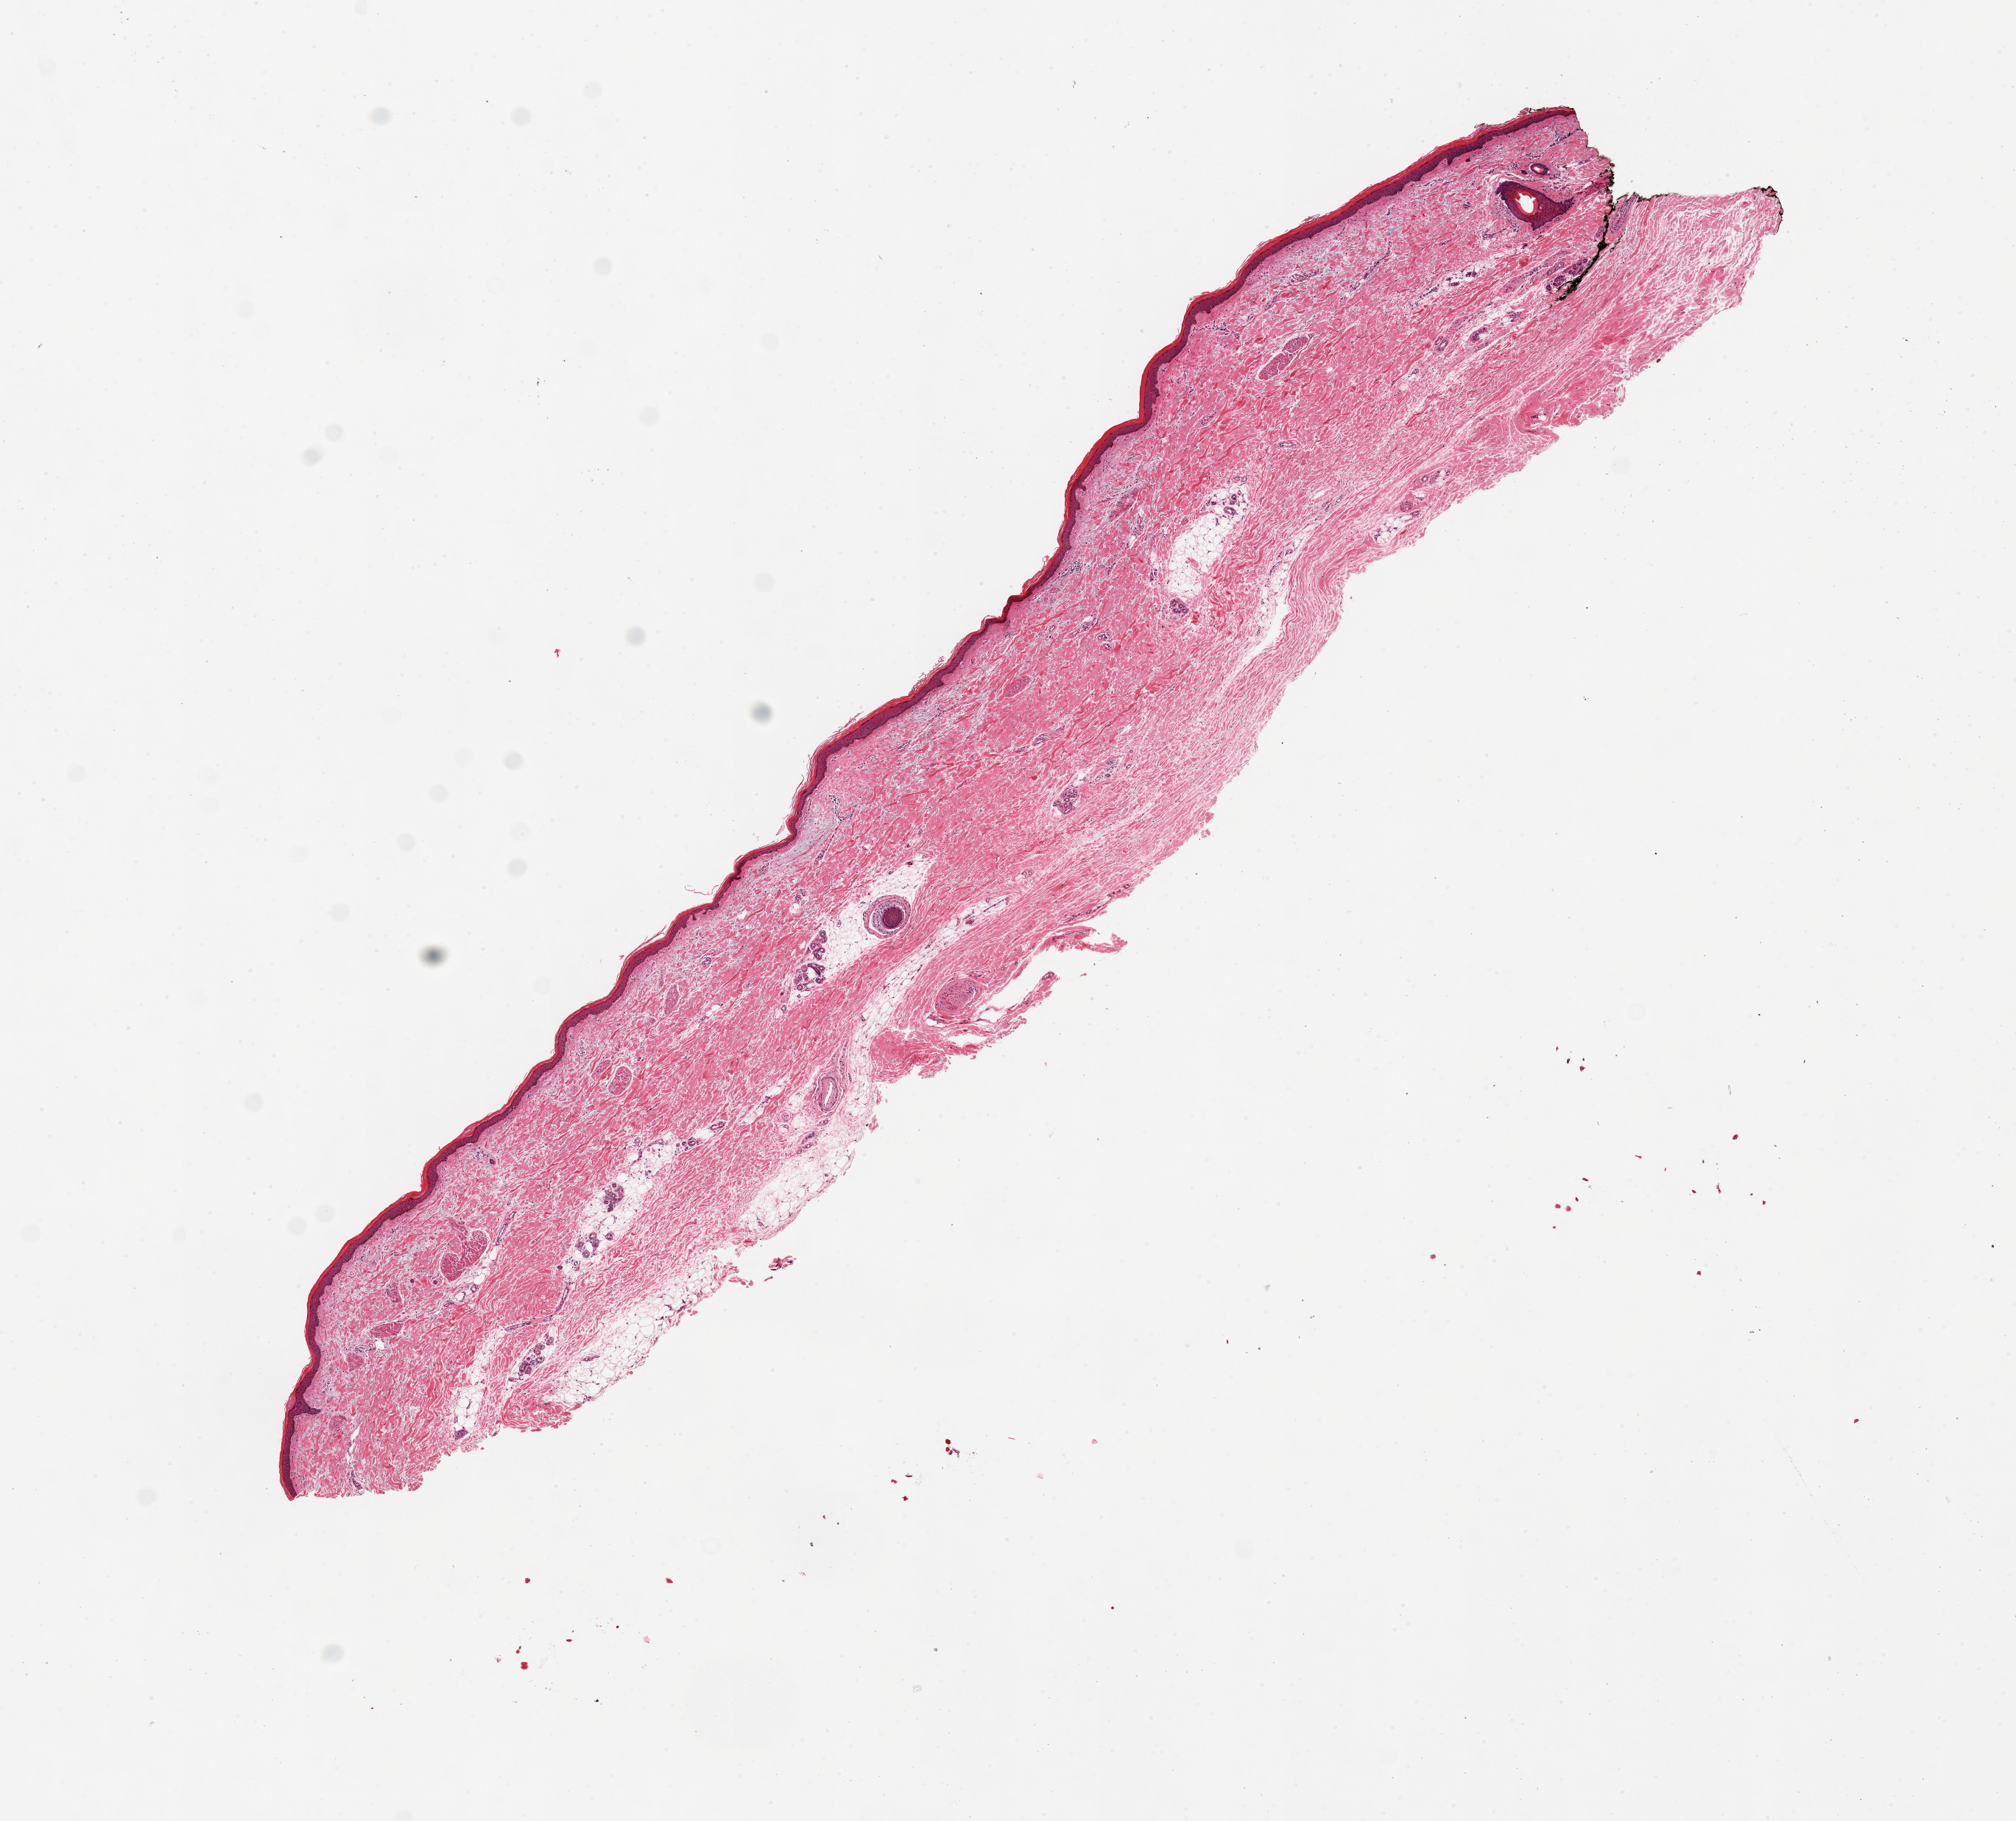
Whole-slide image, hematoxylin and eosin (H&E) stain, brightfield — low-resolution overview of the scanned area, about 10.8 x 9.8 mm. PAXgene-fixed, paraffin-embedded tissue. Section of skin of lower leg (target tissue). Tissue donor sample. Donor: female.
Reviewer comment on this tissue sample: 1 piece, 11x2mm; squamous epithelium is 1-1.%% thickness.